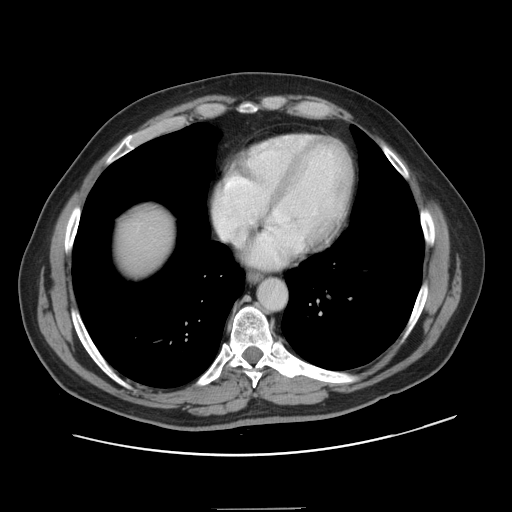
Contrast-enhanced abdominal CT, one axial slice. Slice 141 of 143 in the series (ordered by position). Intravenous contrast given. Soft-tissue window (W 400 / L 40 HU). 2.5 mm slice thickness. 512 × 512 image matrix. Male patient, age 62 years. Case-level facts recorded for this patient, not image findings: diagnosis: colorectal cancer liver metastases, imaged before liver resection; multiple liver metastases: yes; largest metastasis: 2.7 cm; chemotherapy before resection: yes.
Outlined on this slice (outlined manually by an expert reader):
- liver: bounding box <116,211,173,276> (left, top, right, bottom; pixels)
- planned liver remnant (the part of the liver to remain after resection): <116,212,173,276>